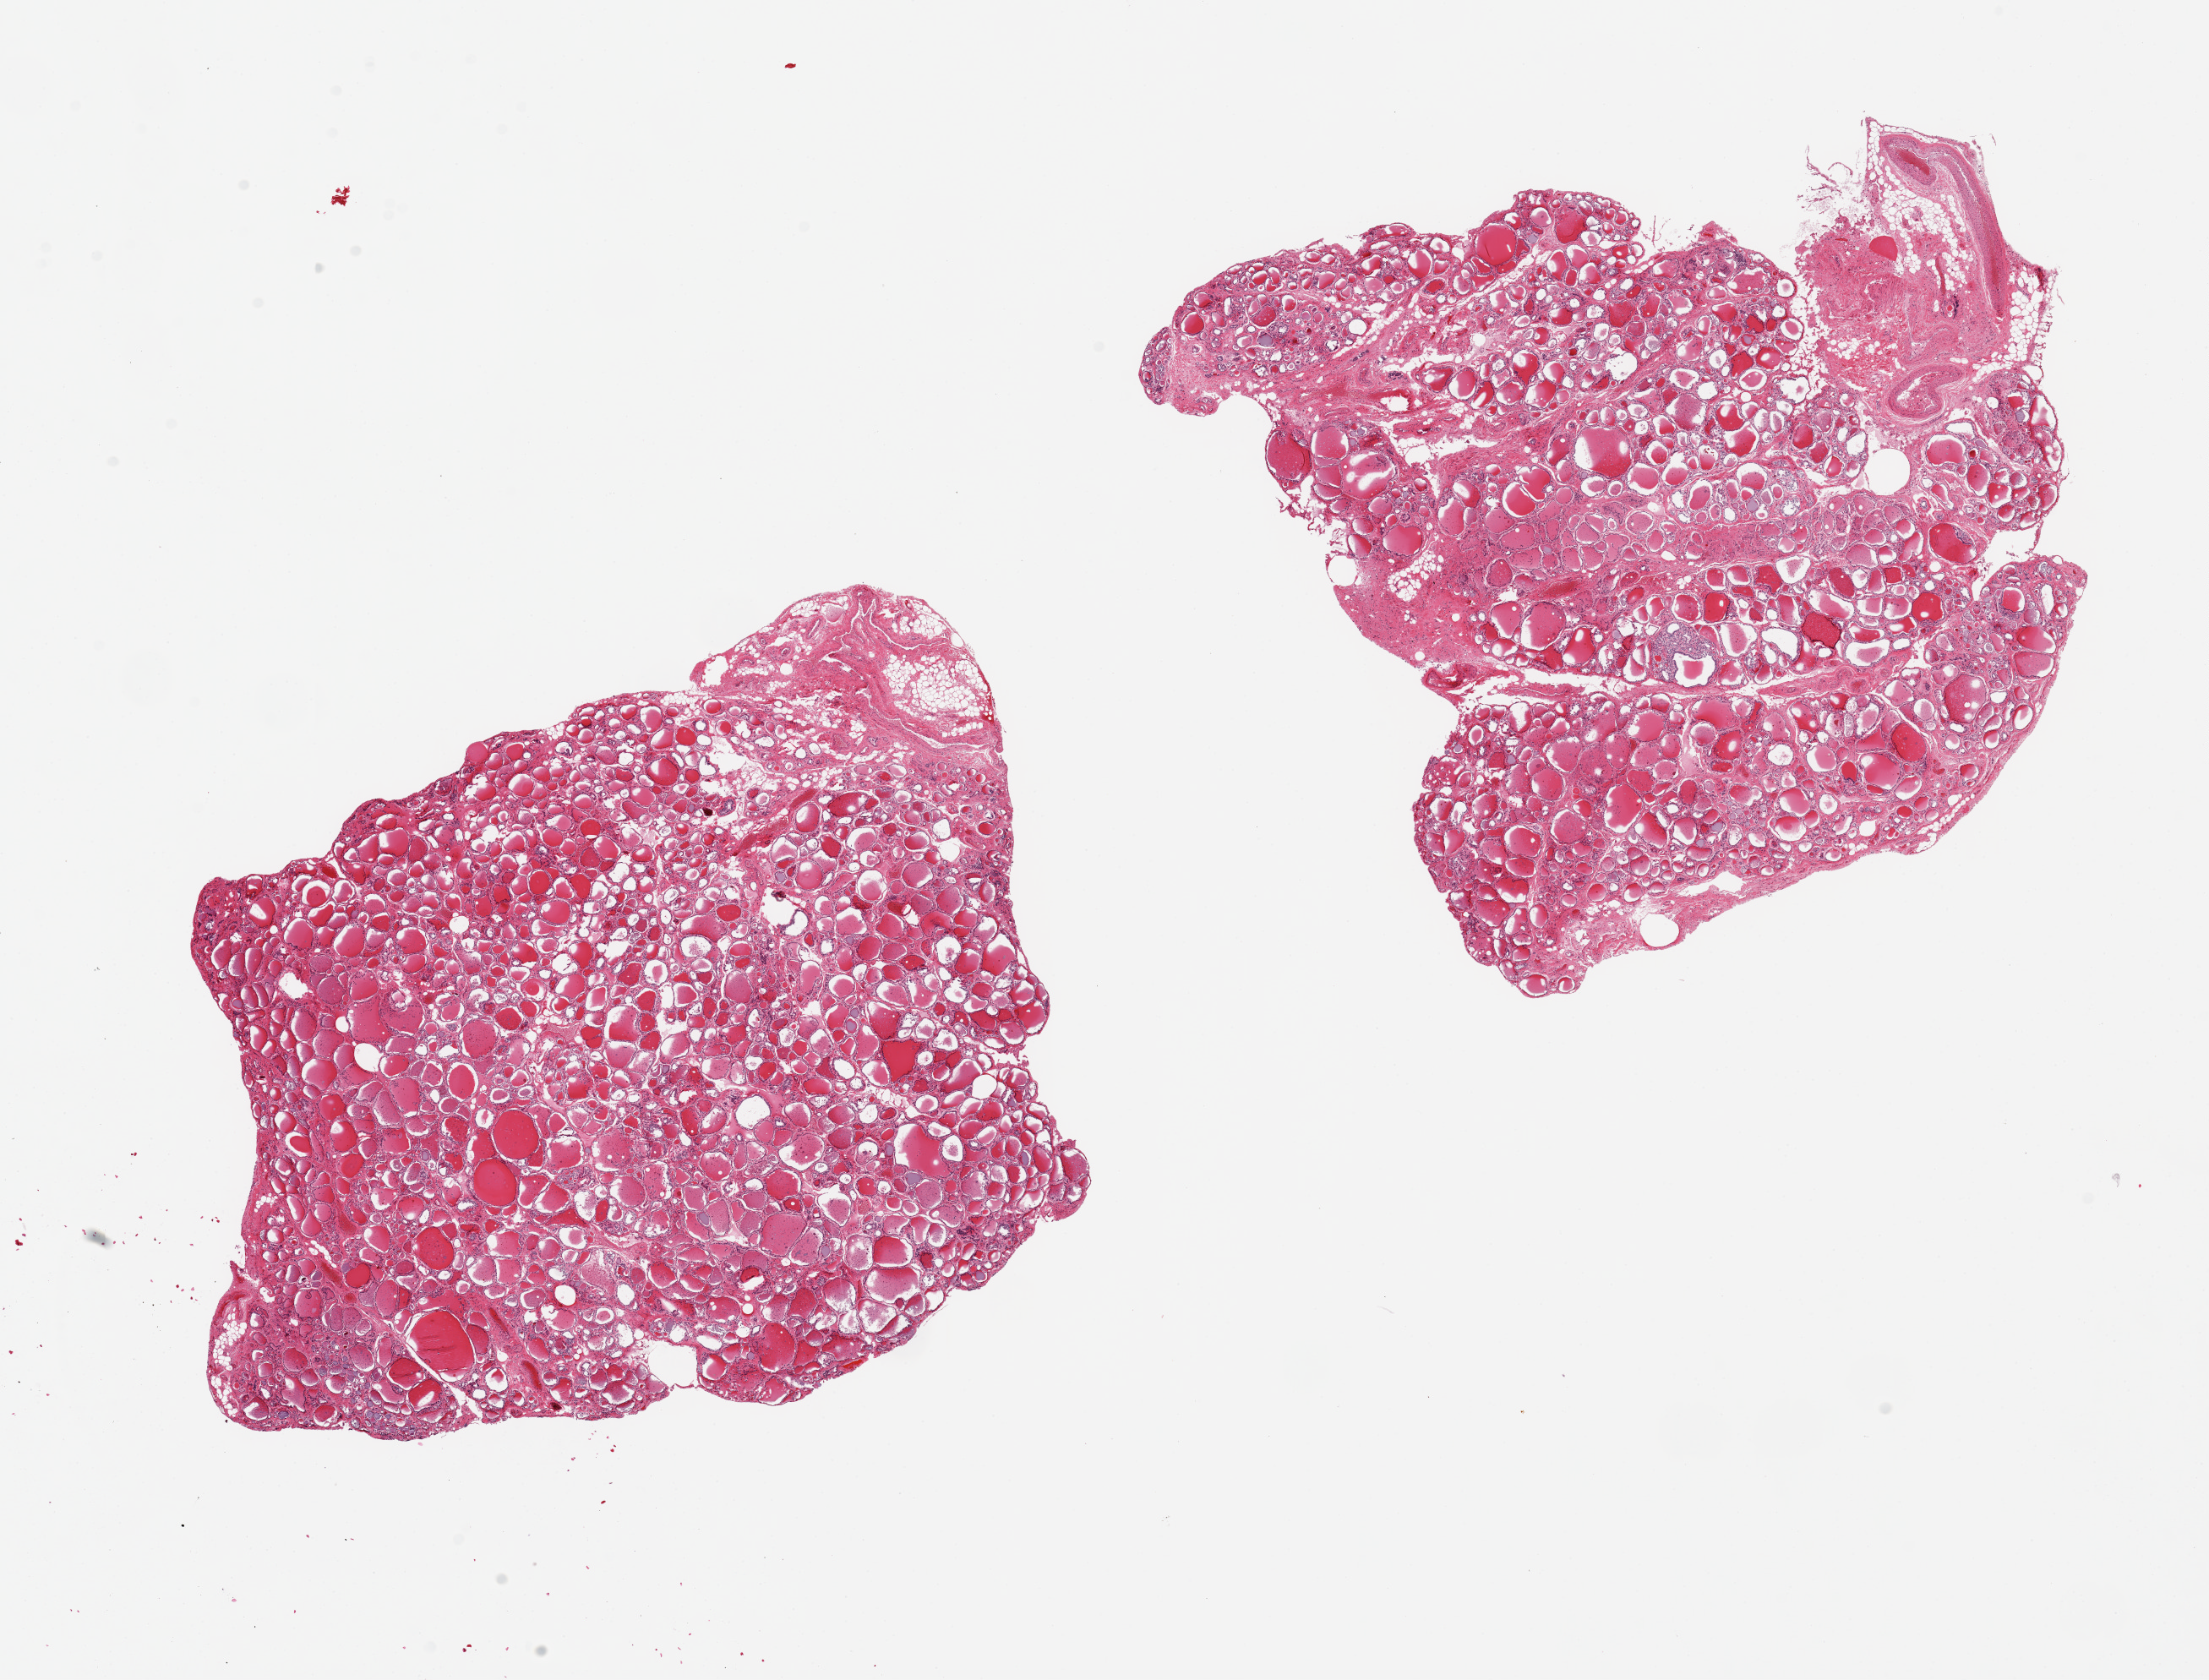
Whole-slide image, haematoxylin and eosin stain — low-resolution overview of the scanned area, about 20.7 x 15.7 mm (acquisition: 20x scan); PAXgene-fixed, paraffin-embedded tissue; target tissue: thyroid; tissue donor sample. Donor: male.
- pathologist's review note for this sample: 2 pieces. 8.5x7 & 8.5x7mm